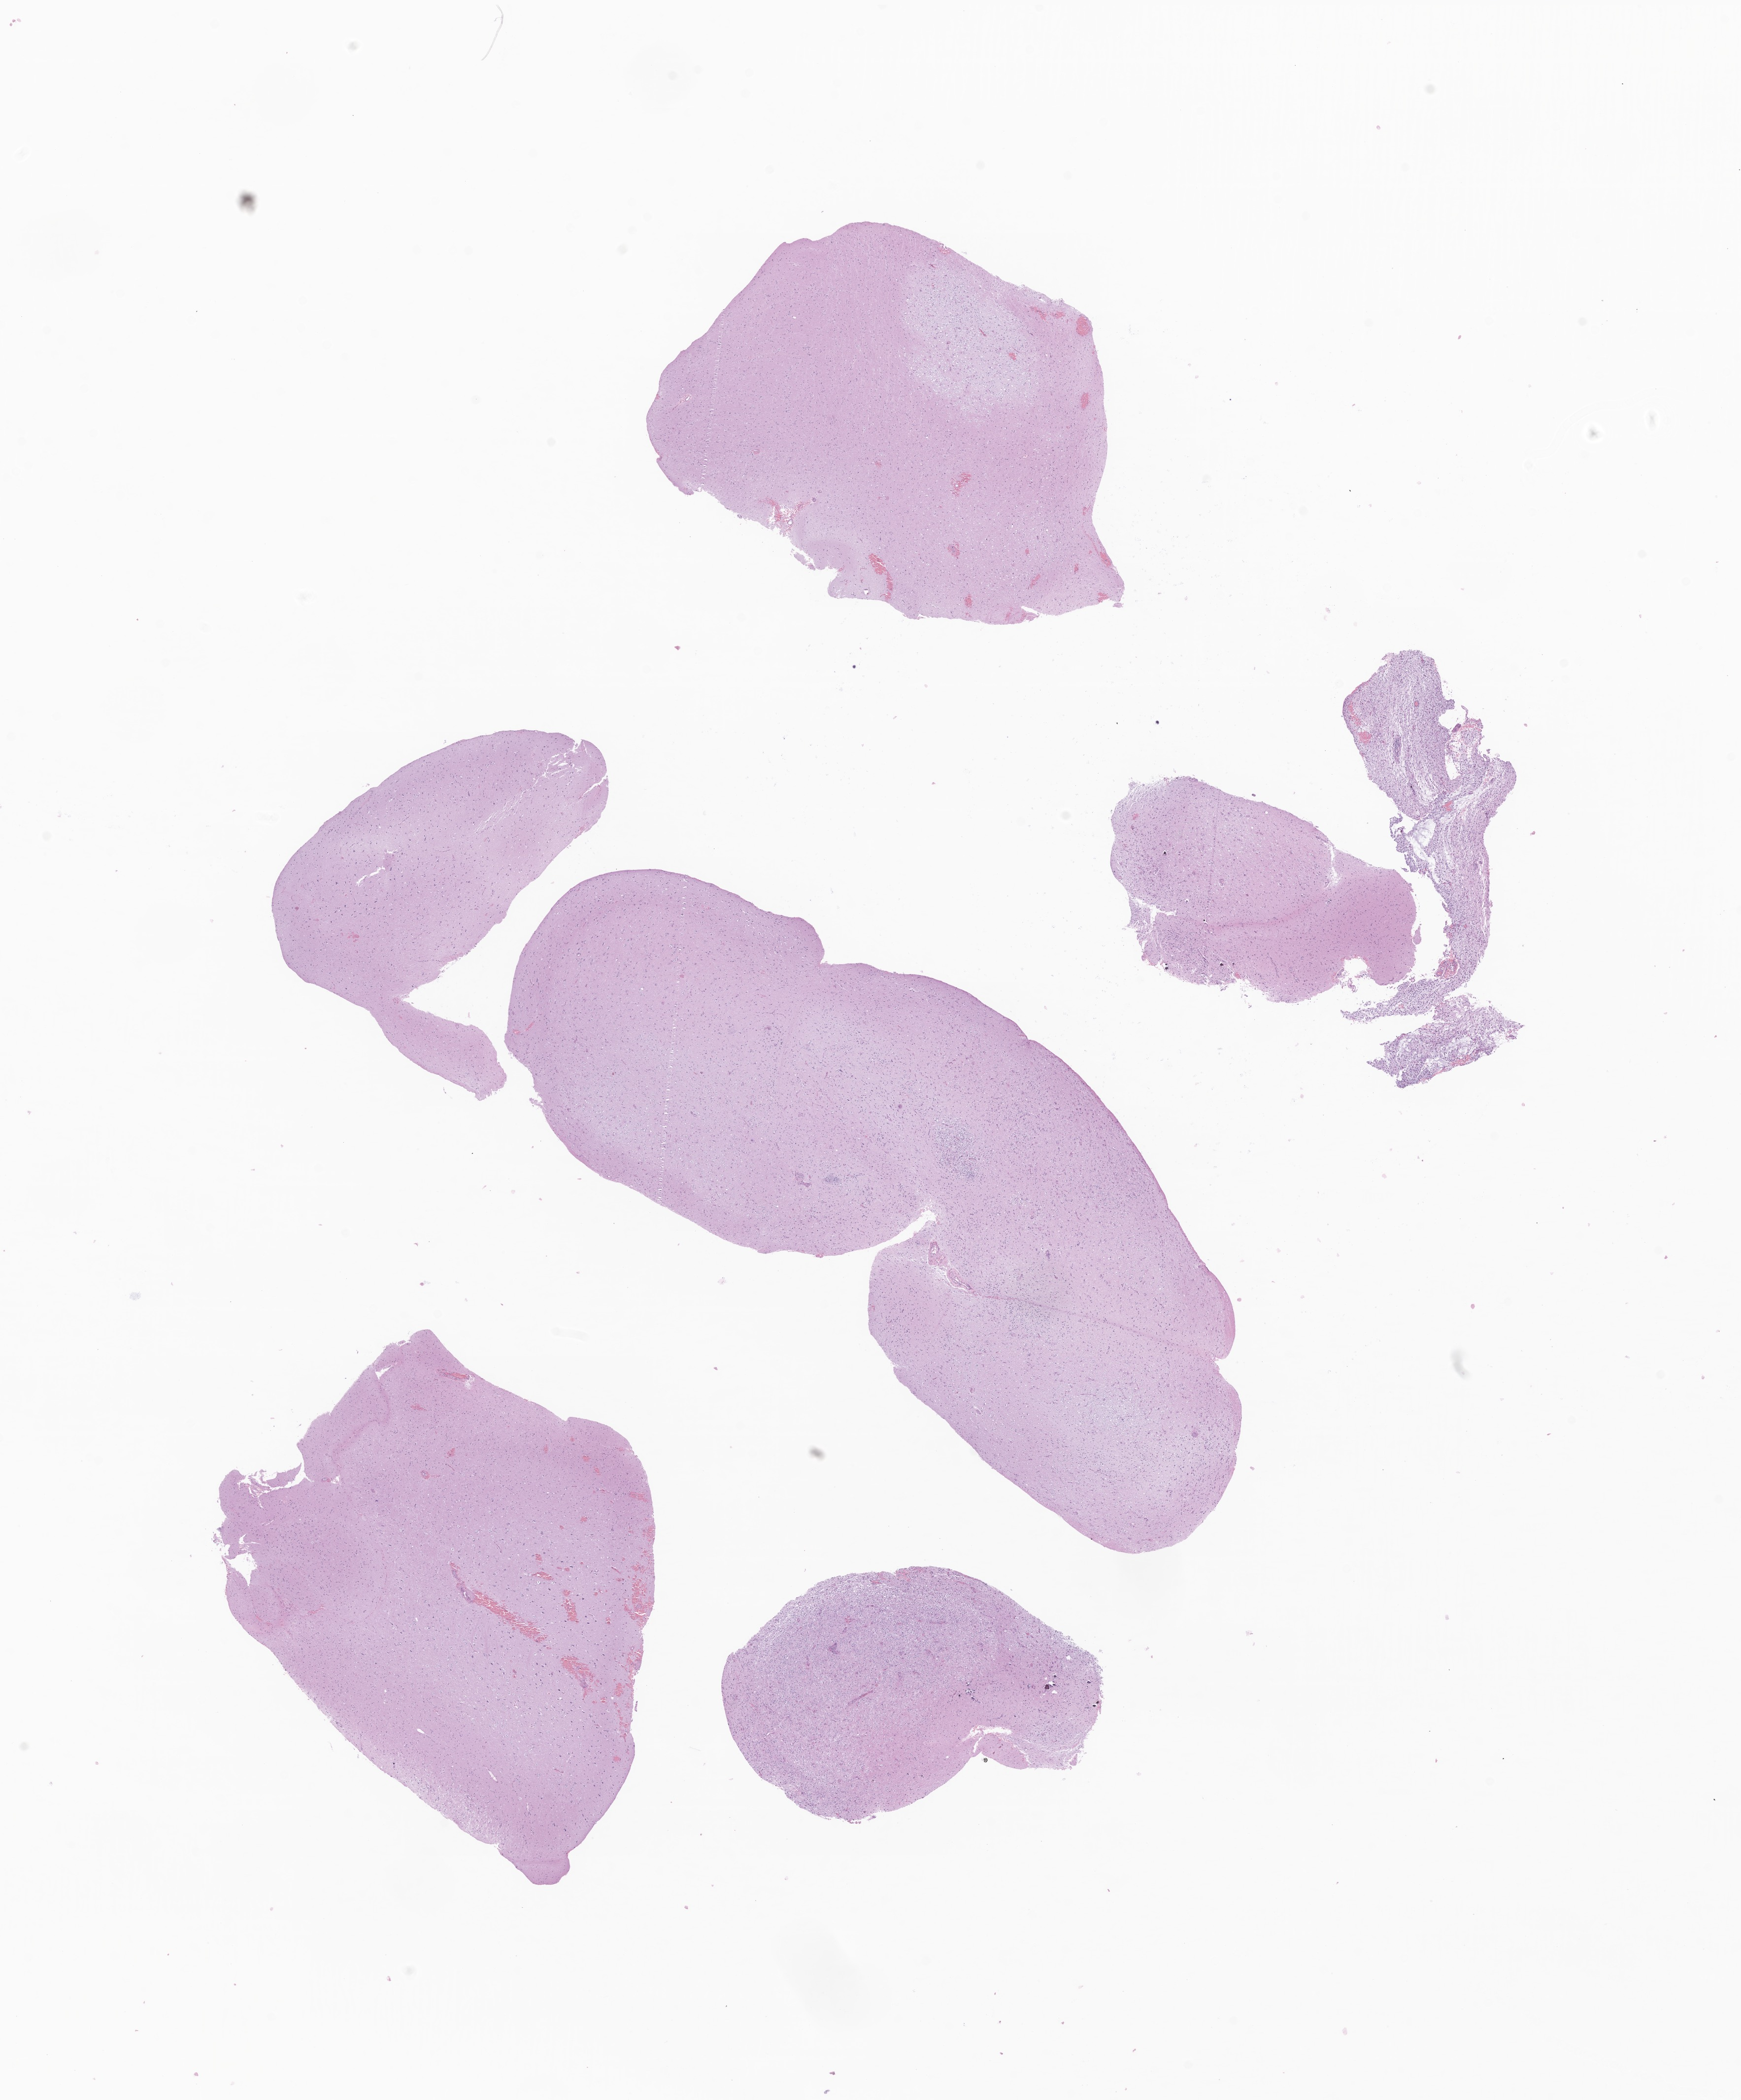
Digitized H&E-stained section of tumor tissue from the brain, low-resolution overview of the scanned area, about 14.9 x 18.0 mm, formalin-fixed, paraffin-embedded (FFPE) tissue. Male patient, age 138 months (11 years 6 months).
Diagnosis (ICD-O-3 morphology term): Neoplasm, uncertain whether benign or malignant.